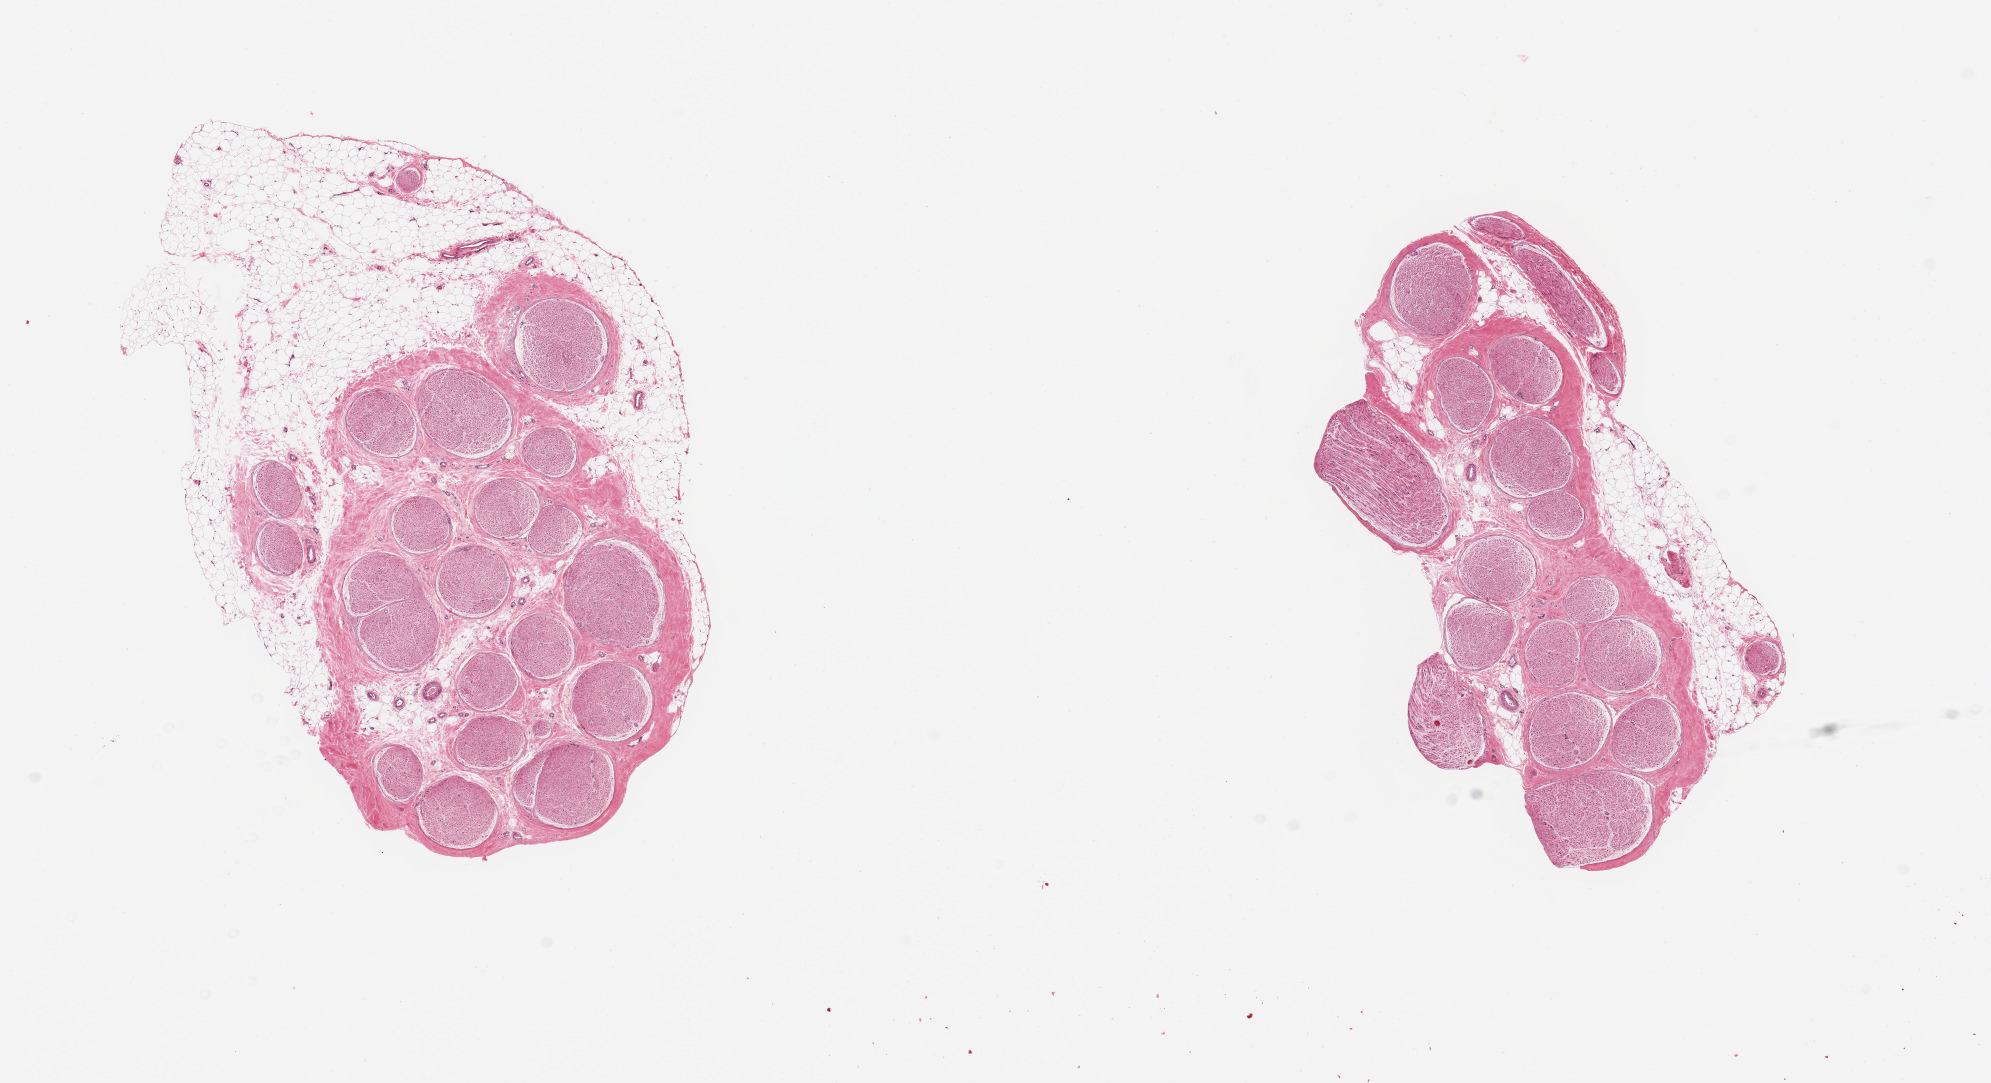
Hematoxylin and eosin (H&E) whole-slide image — whole scanned area (about 15.8 x 8.6 mm) shown as a low-resolution overview; PAXgene-fixed, paraffin-embedded tissue; section of tibial nerve (target tissue); tissue donor sample. Male donor.
Review note (as recorded): 2 pieces, nubbin of adherent fat up to ~2.5mm.